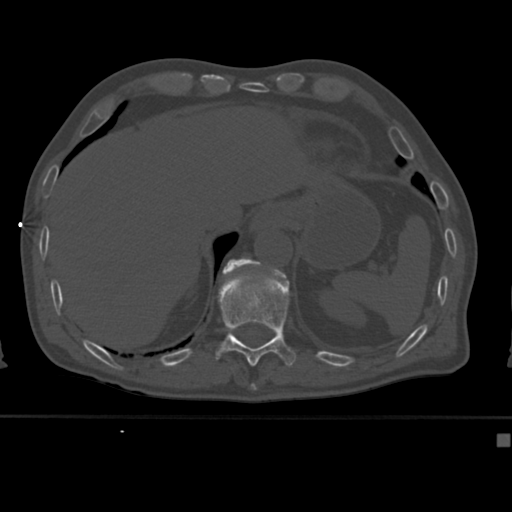
CT including the spine, one axial slice; position 209 of 430 along the scan axis; 120 kVp; bone window (W 1800 / L 400 HU); 512 × 512 image matrix, field of view 337 × 337 mm. Patient: male, 64 years. From the clinical record (not read from this slice): primary cancer: uterus.
Outlined on this slice (semi-automatically segmented with operator editing):
- T11 vertebra: box from (x=215, y=265) to (x=296, y=367) px
- T12 vertebra: (x=222, y=258)–(x=254, y=275)